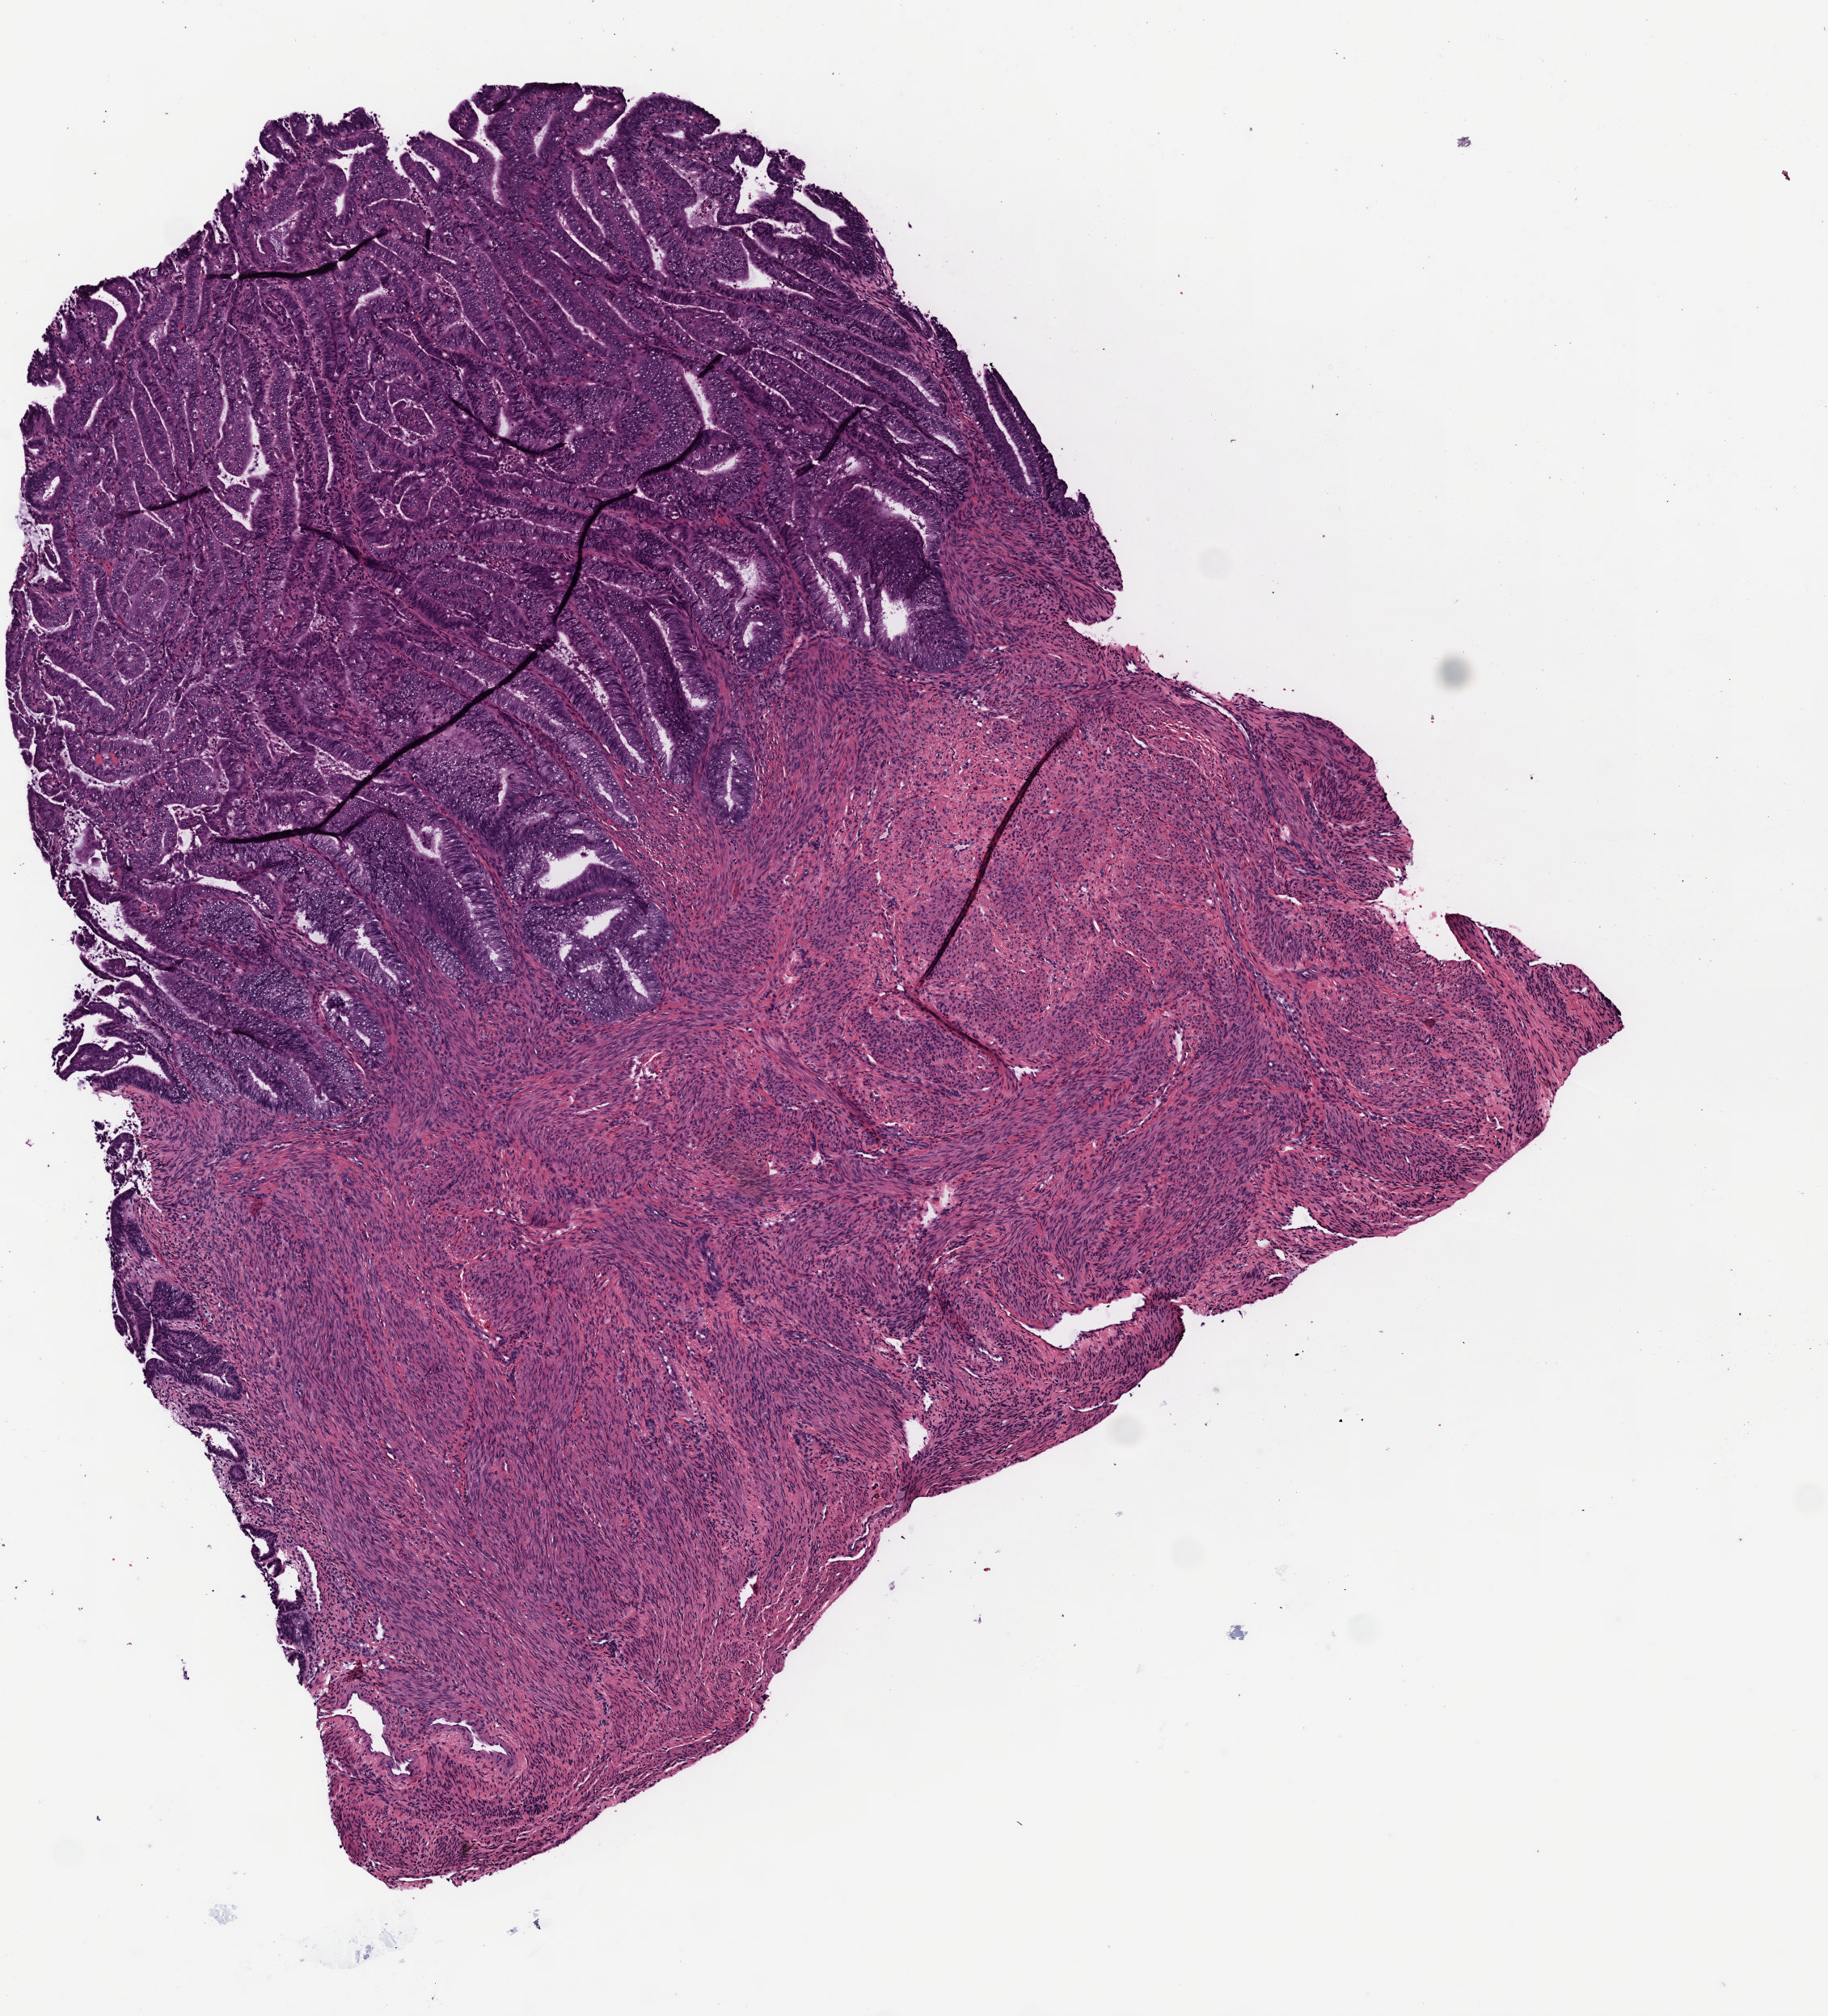
Digitized Hematoxylin and eosin (H&E) stained tissue section (whole slide) — whole scanned area (about 4.4 x 4.9 mm, slide scanned at 40x) shown as a low-resolution overview. Formalin-fixed paraffin-embedded (FFPE) diagnostic section. Sample: primary tumour, uterus. Patient: female, age at initial diagnosis 62 years. Histologic grade: G2 (moderately differentiated).
Histologic diagnosis: Endometrioid adenocarcinoma, NOS (endometrium). FIGO stage: IA.